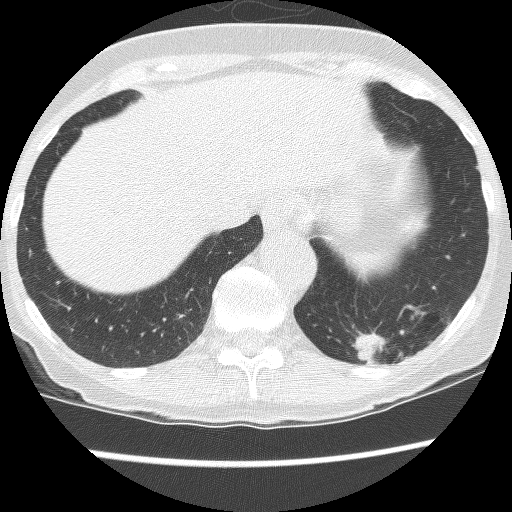
Axial slice from a low-dose chest CT screening exam, third annual screen, lung window (W 1500 / L -600 HU), 2.5 mm slice thickness, 120 kVp, slice 103 of 130 in the series, 512 × 512 image matrix. Female, age 61 years at enrolment. Current smoker at enrolment.
Expert-annotated lung lesion, bounding box (x1, y1, x2, y2) in pixels: (336, 295, 441, 386). The screening reader recorded 2 non-calcified nodules or masses ≥4 mm on this exam (left lower lobe, left lower lobe); which of them this box marks is not recorded. Participant outcome: lung cancer diagnosed 166 days after this screen — non-small cell carcinoma, left lower lobe, poorly differentiated (G3), stage IB (AJCC 6th edition), 100 mm at pathology.